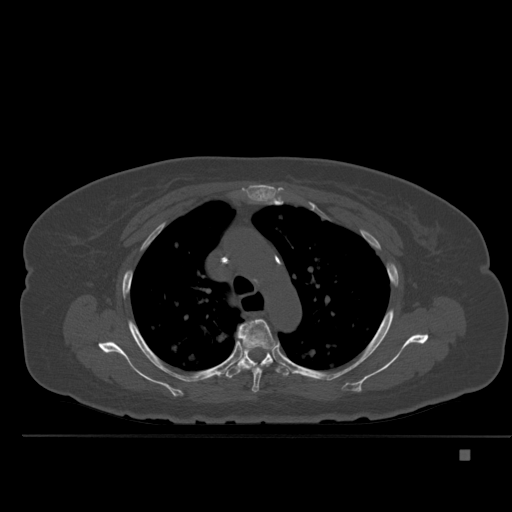
CT including the spine, one axial slice. Slice 361 of 477 in the series (ordered by position). Bone window (W 1800 / L 400 HU). 1.5 mm slice thickness. 512 × 512 image matrix, field of view 422 × 422 mm. Patient: female, 74 years. Case-level facts recorded for this patient, not image findings: primary cancer: colon.
Outlined on this slice (semi-automatically segmented with operator editing):
- T4 vertebra: box from (x=236, y=319) to (x=278, y=393) px
- T5 vertebra: (x=225, y=337)–(x=289, y=379)